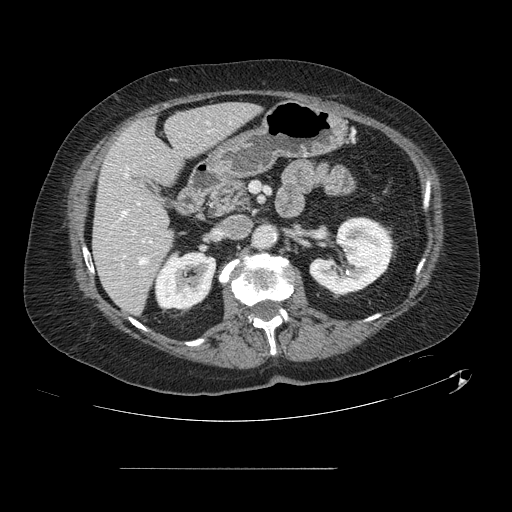
Contrast-enhanced abdominal CT, one axial slice. Slice 54 of 148 in the series (ordered by position). Intravenous contrast given. Soft-tissue window (W 400 / L 40 HU). 2.5 mm slice thickness. 512 × 512 image matrix, field of view 439 × 439 mm. Female patient, age 75 years. From the clinical record (not read from this slice): diagnosis: colorectal cancer liver metastases, imaged before liver resection; multiple liver metastases: no; largest metastasis: 2.4 cm; disease in both lobes: no.
Annotated regions visible in this slice (outlined manually by an expert reader):
- hepatic veins: bounding box <121,174,148,265> (left, top, right, bottom; pixels)
- liver: <94,105,258,314>
- planned liver remnant (the part of the liver to remain after resection): <94,105,258,314>
- portal vein (with intrahepatic branches): <124,203,140,257>